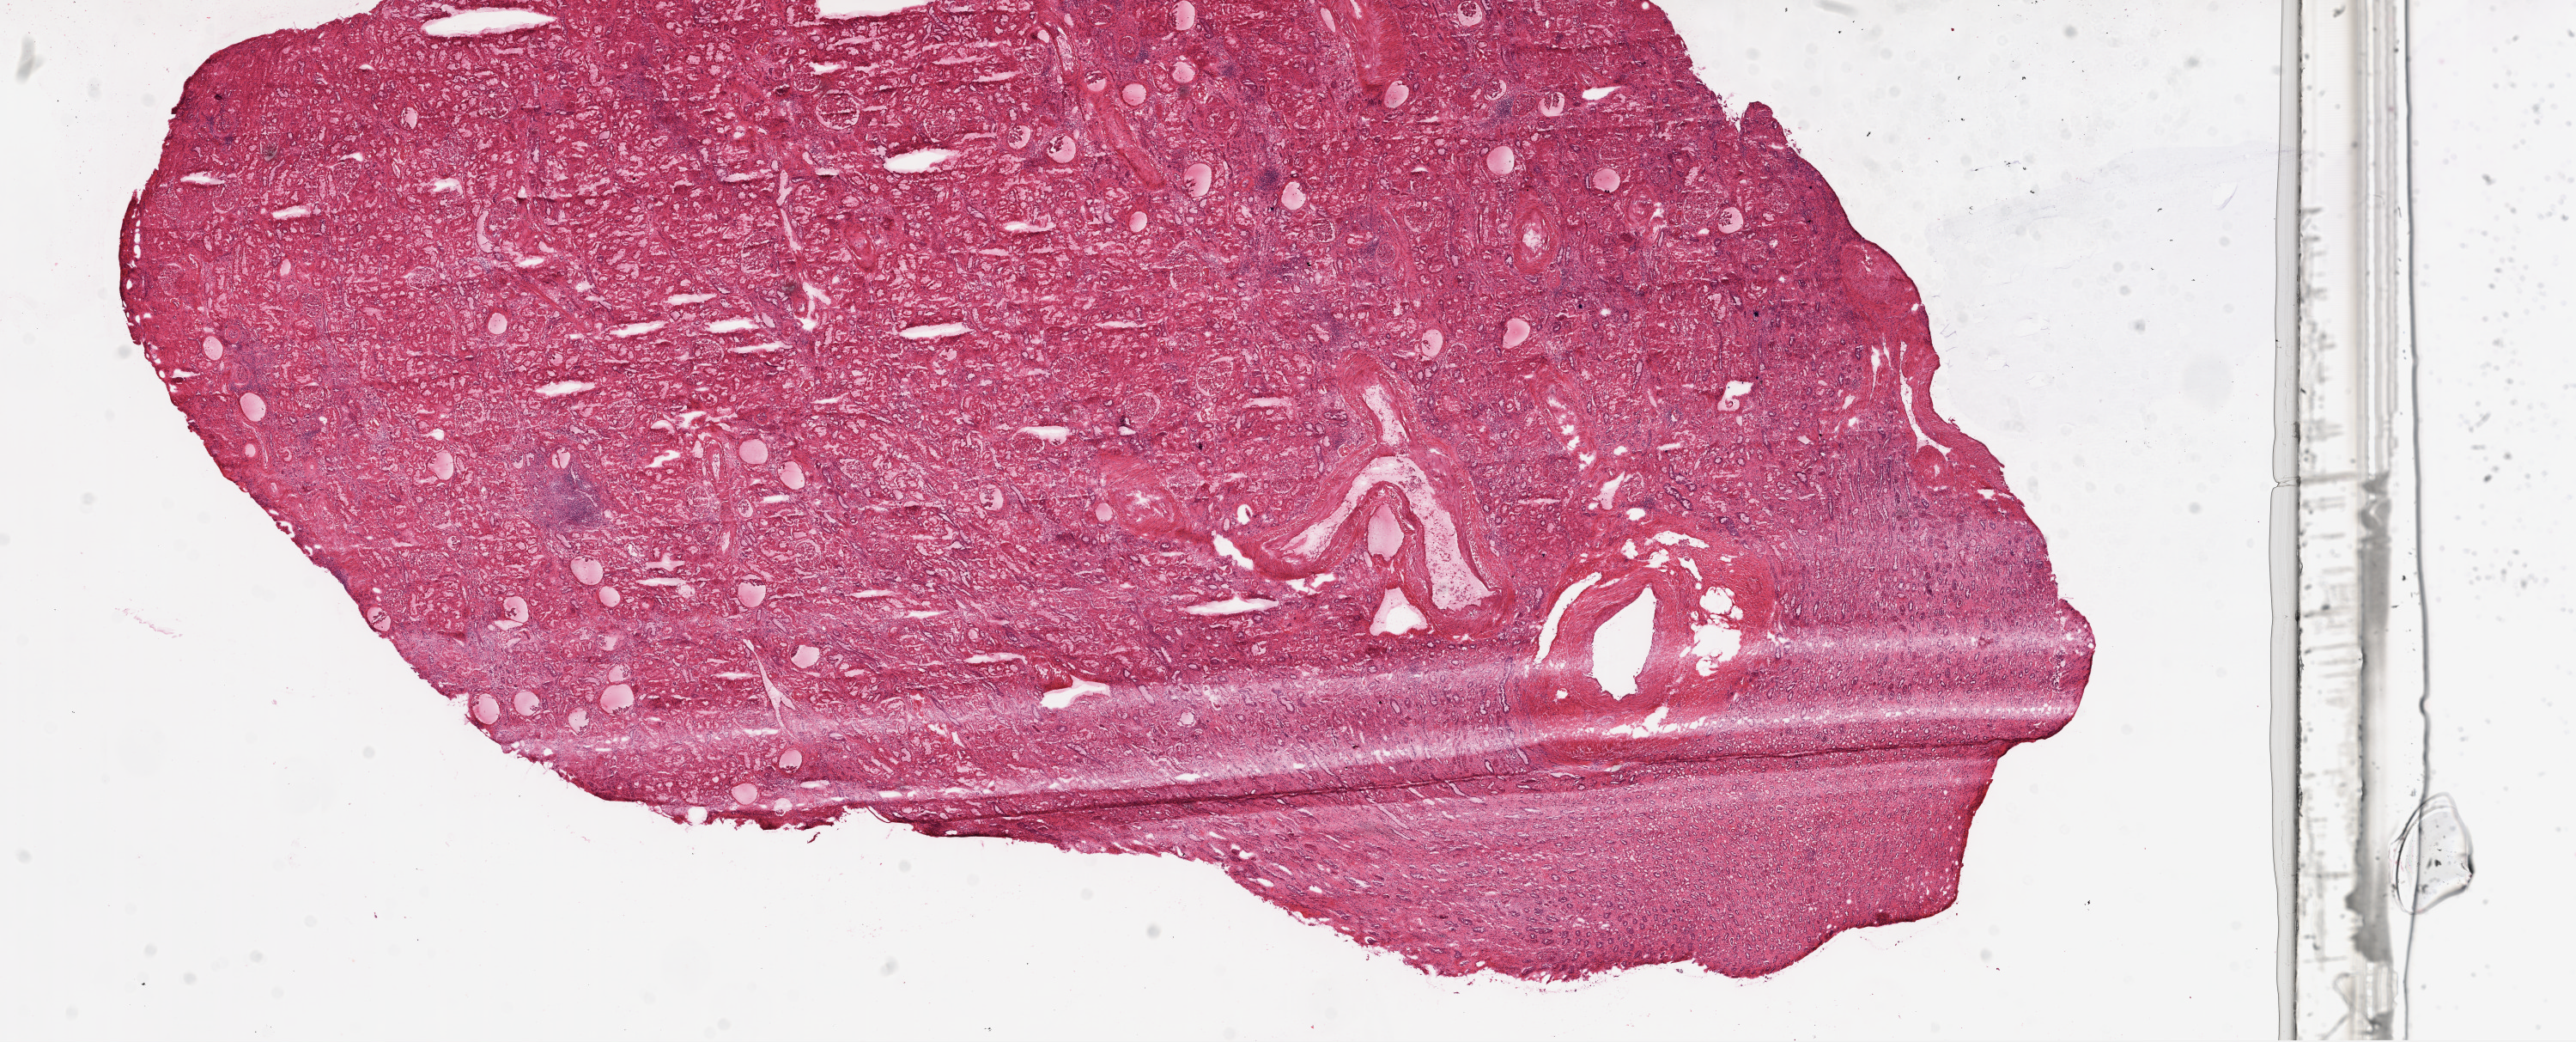
Digitized H&E tissue section (whole slide) — a low-resolution overview of the entire scanned area, about 24.1 x 9.7 mm, frozen section from the top of the tissue portion, solid tissue normal (non-tumour tissue) sample from the kidney. Patient: male, age at initial diagnosis 49 years.
This section: solid tissue normal sample (biorepository sample class). Patient diagnosis: Clear cell adenocarcinoma, NOS.